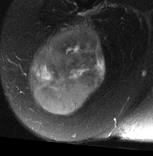
MRI of an extremity soft-tissue mass, one axial slice; slice 29 of 77 in the series (ordered by position); T2-weighted fat-saturated; MR volume resampled by the dataset authors to the PET/CT grid (not the native acquisition matrix); 3.27 mm slice thickness; 153 × 156 image matrix, field of view 149 × 152 mm. Female patient. Case-level facts recorded for this patient, not image findings: histological type: synovial sarcoma; grade: intermediate; site of the primary tumour: right buttock.
Outlined on this slice (expert contour drawn on MRI and transferred to this co-registered scan by the dataset authors):
- gross tumour volume including surrounding oedema: bounding box <28,18,106,116> (left, top, right, bottom; pixels)
- gross tumour volume (mass): <28,27,106,116>